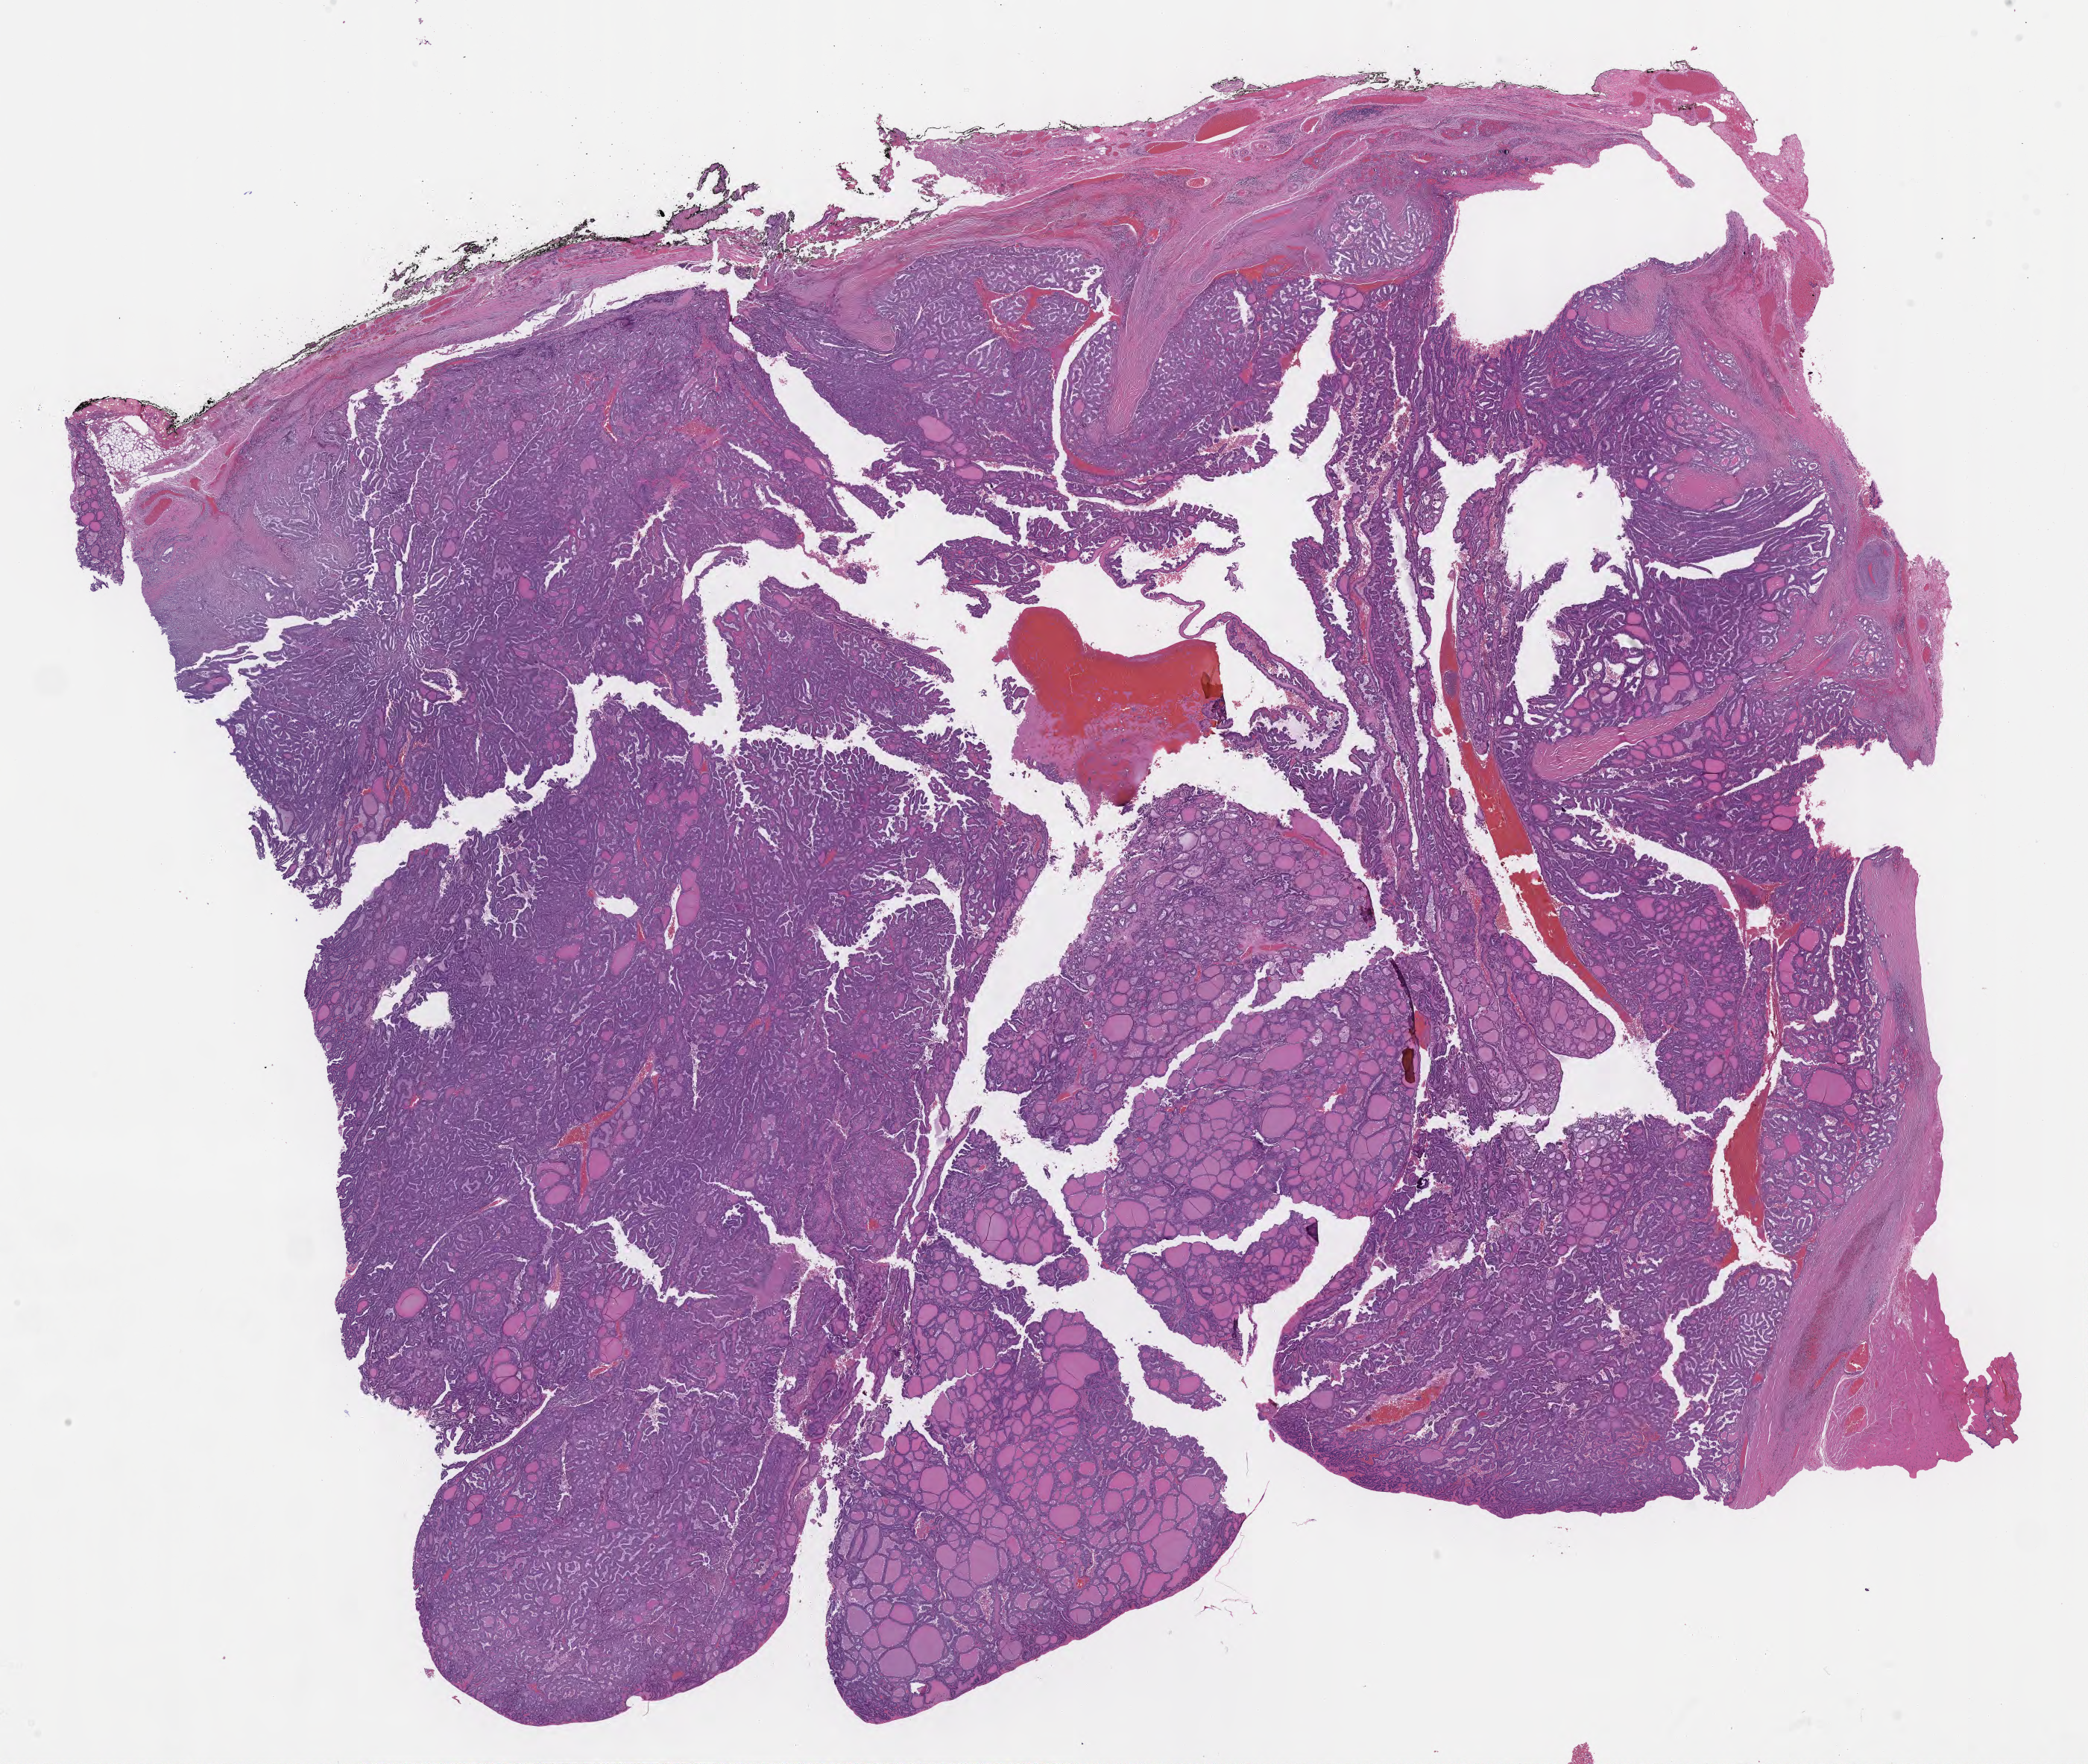
Whole-slide image, hematoxylin and eosin (H&E) stain of tumor tissue from the thyroid — shown as a low-resolution overview of the whole scanned area (about 22.6 x 19.1 mm). Formalin-fixed paraffin-embedded section. Patient male; age 307 months (25 years 7 months).
- recorded diagnosis: Papillary carcinoma, NOS